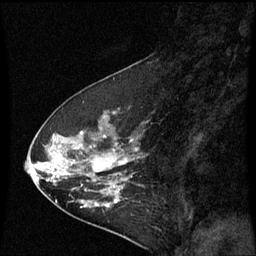
Breast MRI (dynamic contrast-enhanced), one sagittal slice. Position 24 of 60 along the scan axis. Dynamic contrast-enhanced series, image 2 of 3 at this slice position (ordered by acquisition). 1.5 T. TE 4.2 ms, TR 8.9 ms. 2 mm slice thickness. 256 × 256 image matrix, field of view 200 × 200 mm. Female patient, age 53 years. From the clinical record (not read from this slice): setting: breast cancer imaged before/during neoadjuvant chemotherapy; receptor status: HR-positive, HER2-negative.
Outlined on this slice (semi-automatically segmented with operator editing):
- analysis volume of interest (the breast-tissue region the enhancement analysis was run in; not a lesion): bounding box [x1, y1, x2, y2] px = [32, 102, 145, 221]
- tumour enhancement mask (voxels above the 70 % enhancement threshold inside the analysis volume of interest): [52, 158, 127, 207]